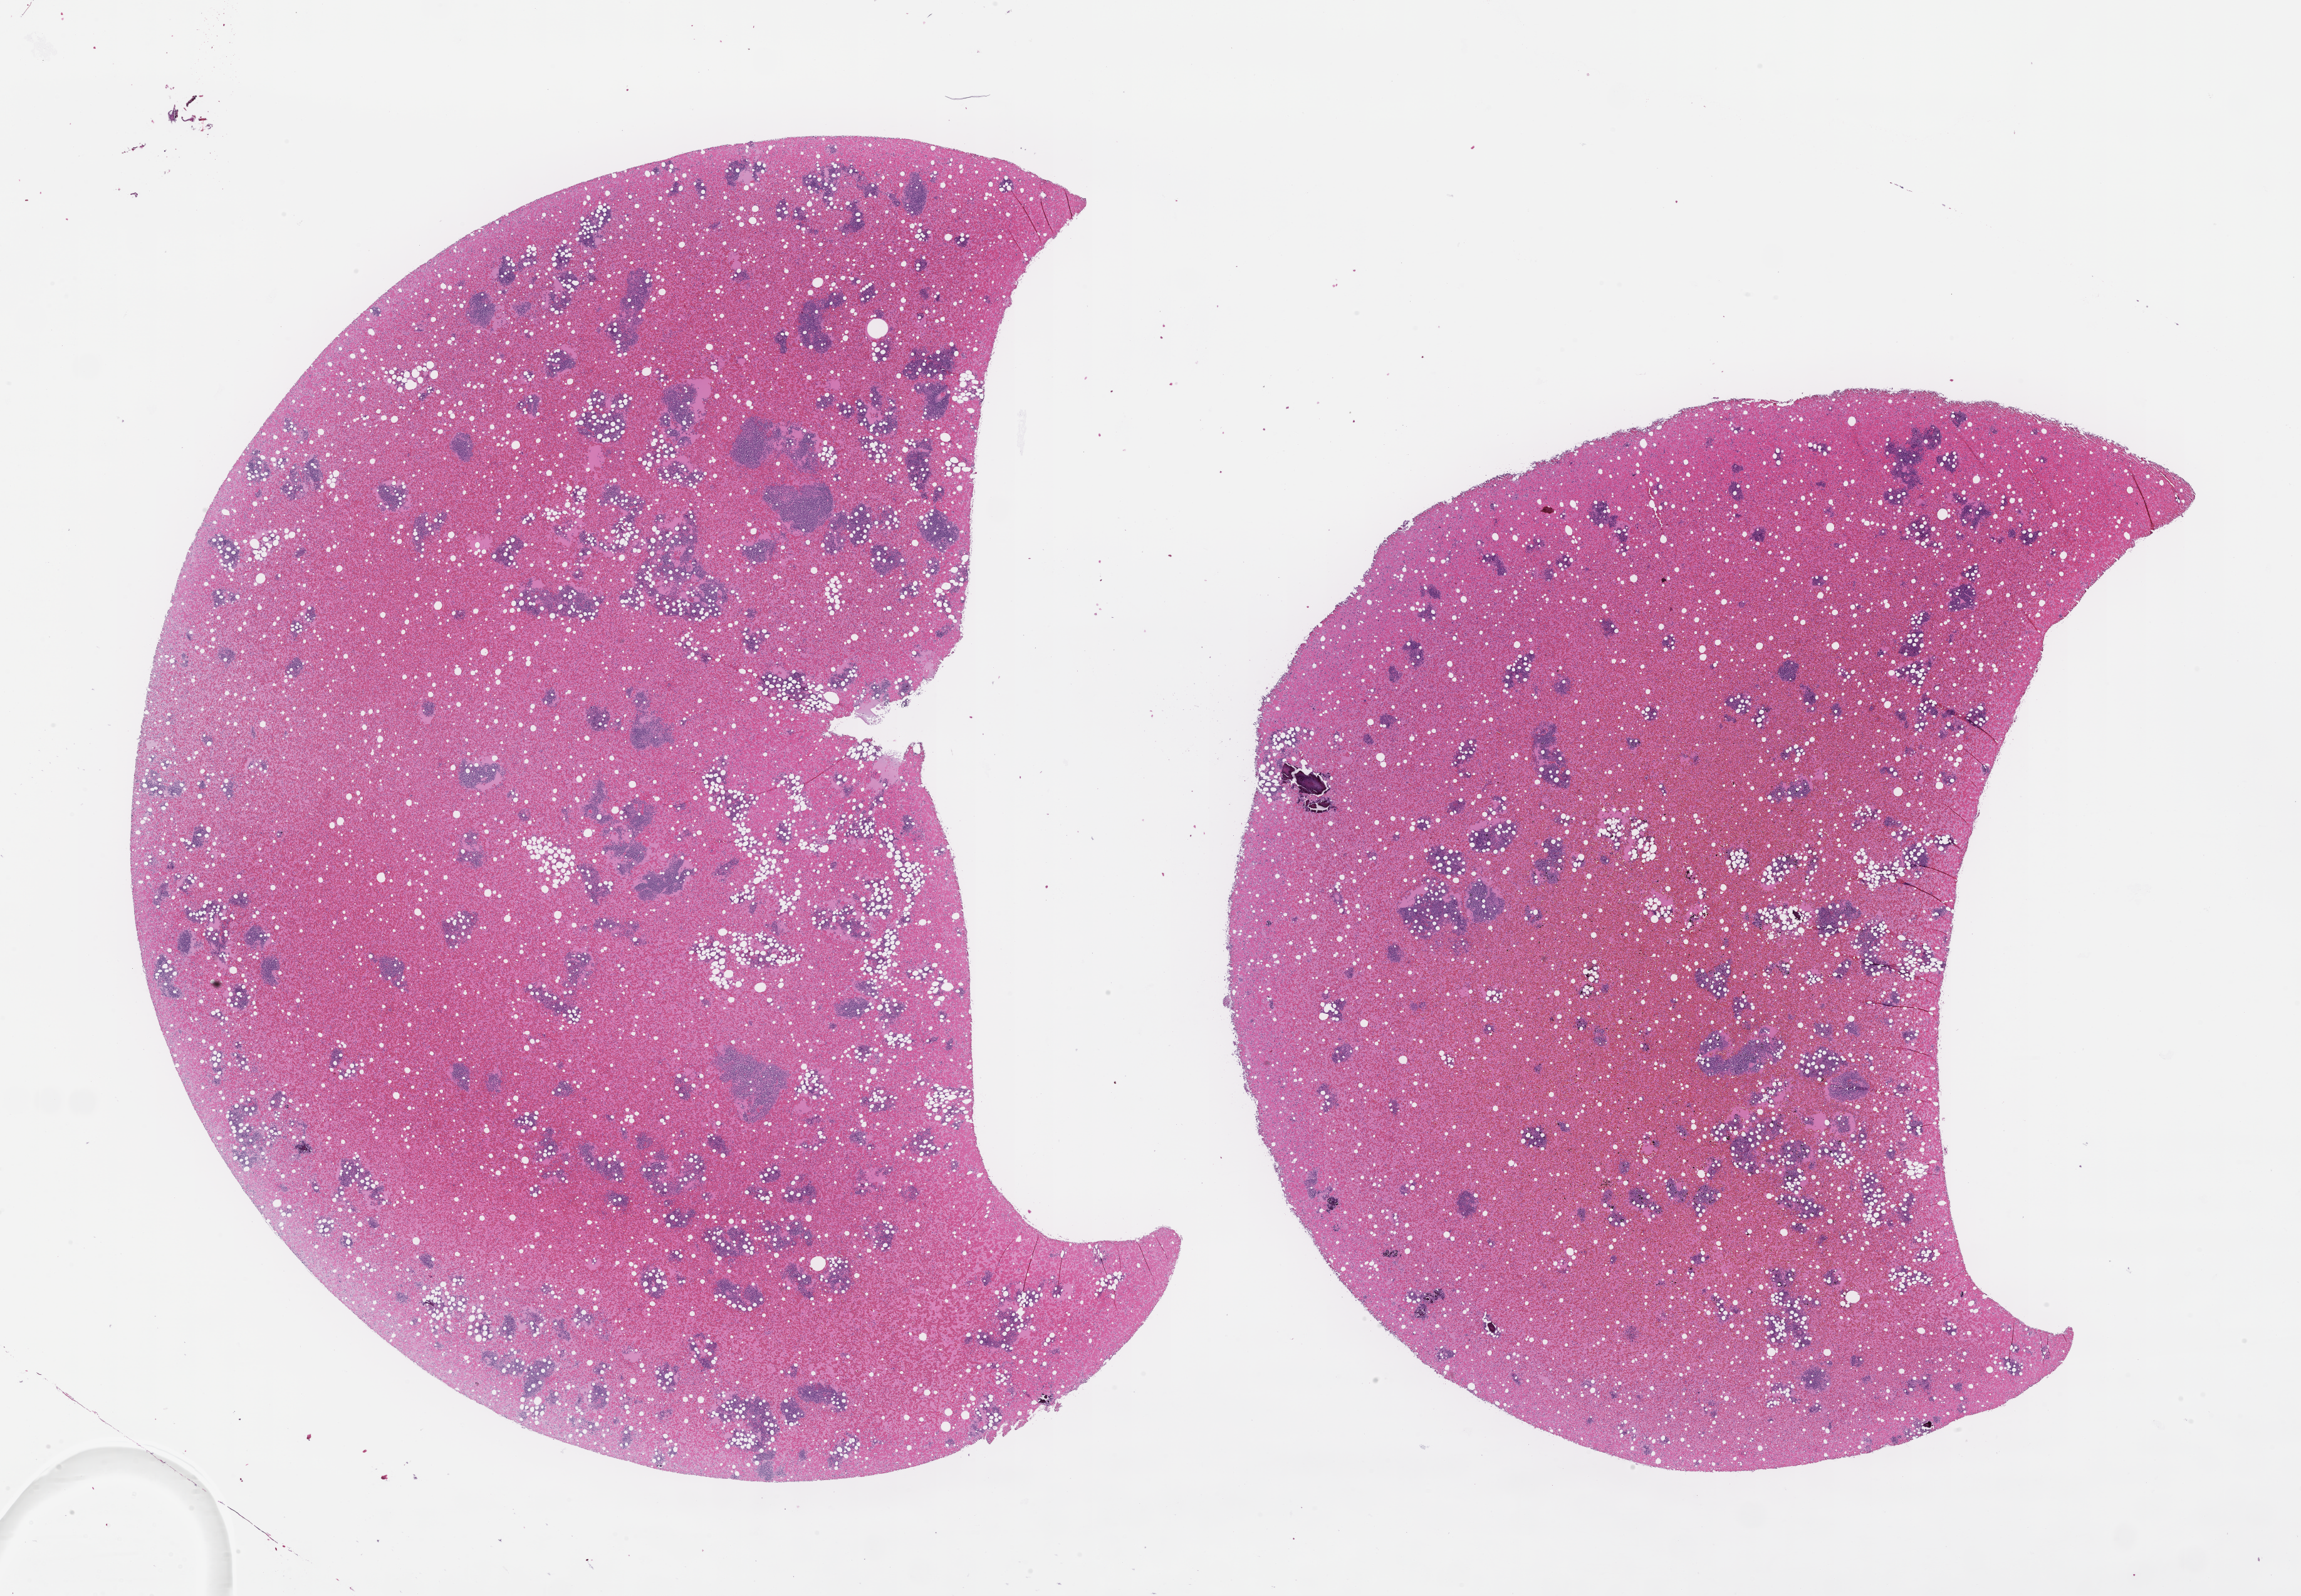
Whole-slide image, H&E stain — low-resolution overview of the scanned area, about 29.7 x 20.6 mm. Formalin-fixed paraffin-embedded section. Tissue site: bone marrow. Patient: male.
This section: primary tumour tissue. Diagnosis: Plasma Cell Myeloma.